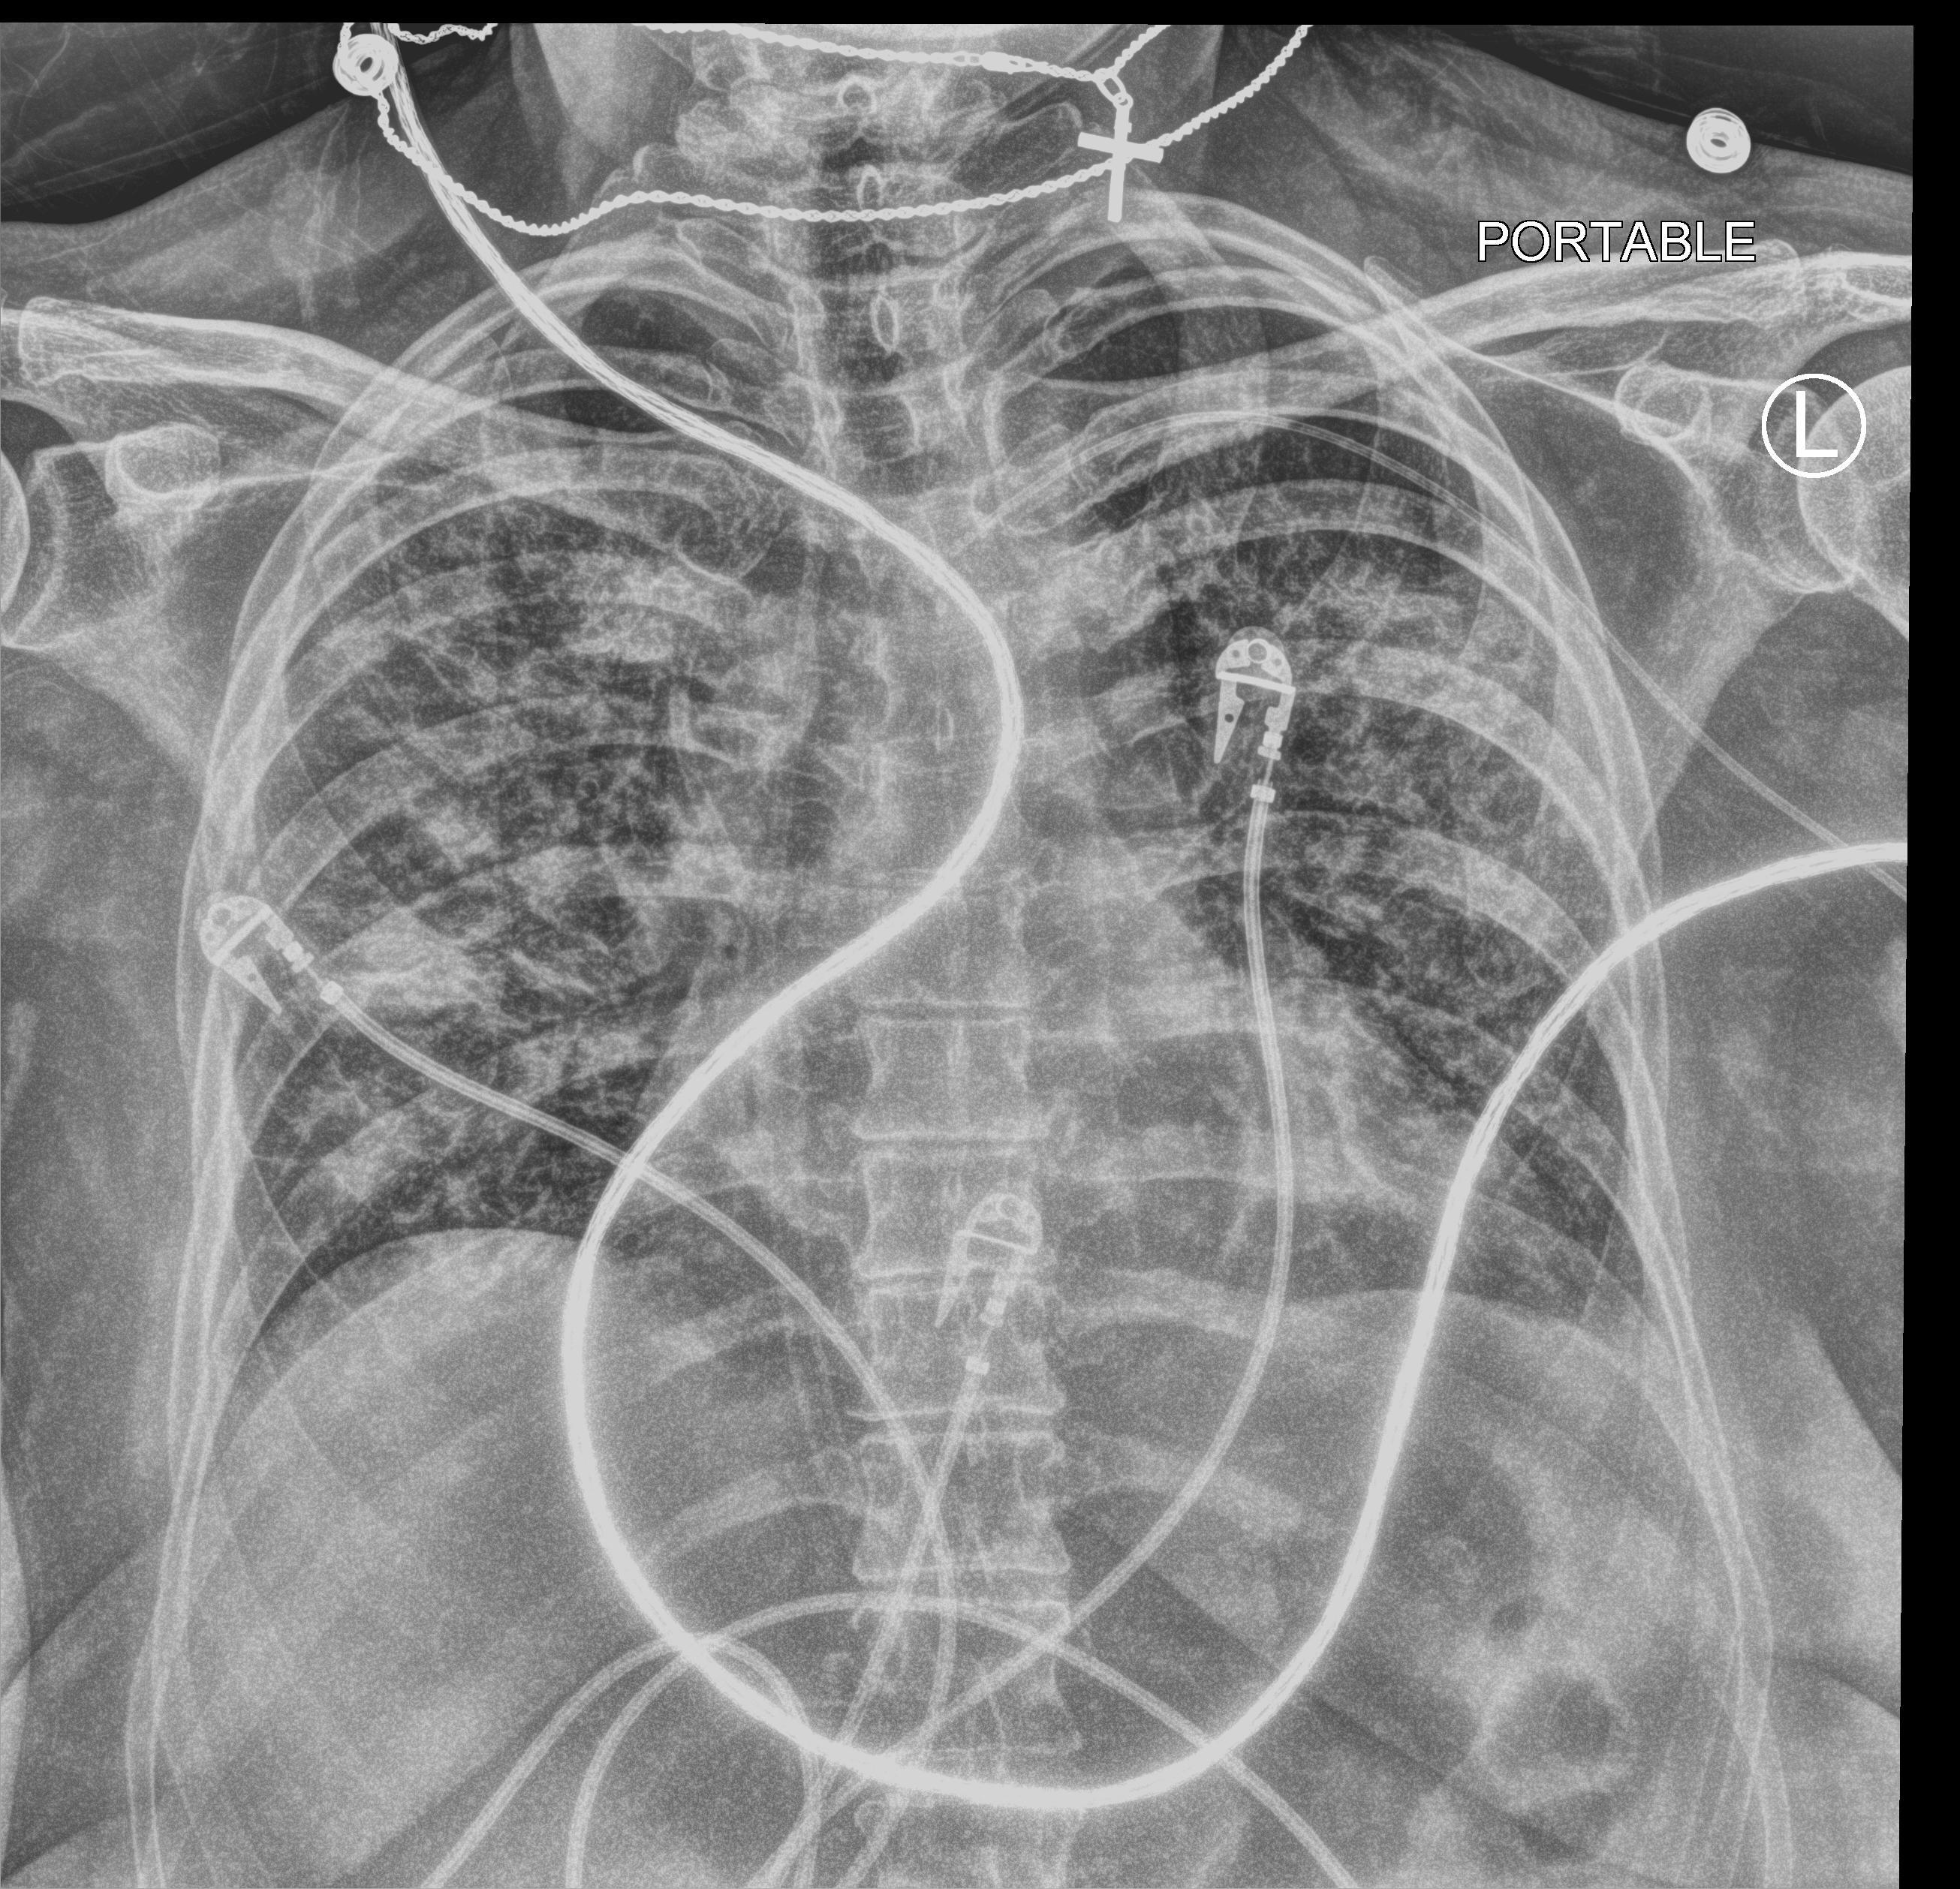
Chest X-ray (portable). Patient hospitalised with COVID-19; female, aged 18–59 years.
Admission-level facts for this patient (not findings on this image; timing relative to this image not recorded): length of hospital stay: 20 days; hypertension (admission record): no; mechanically ventilated during this hospital stay: yes.